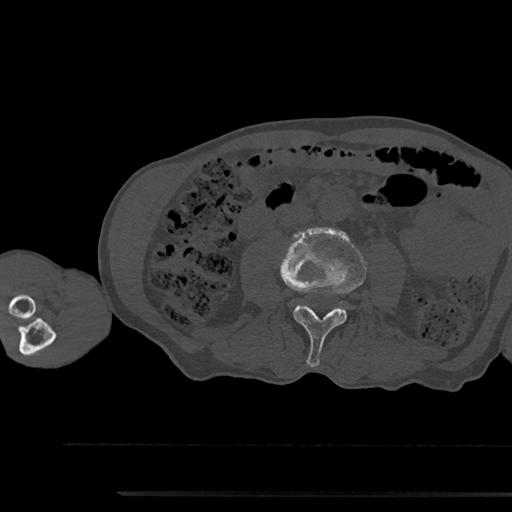
CT including the spine, one axial slice. Slice 469 of 797 in the series (ordered by position). Reconstruction kernel Br40s/3. 120 kVp. Bone window (W 1800 / L 400 HU). 0.5 mm slice thickness. 512 × 512 image matrix, field of view 367 × 367 mm. Patient: male, 79 years. Case-level facts recorded for this patient, not image findings: primary cancer: prostate.
Structures marked on this image (semi-automatic segmentation, software-assisted and operator-edited):
- L3 vertebra: box from (x=280, y=227) to (x=367, y=367) px